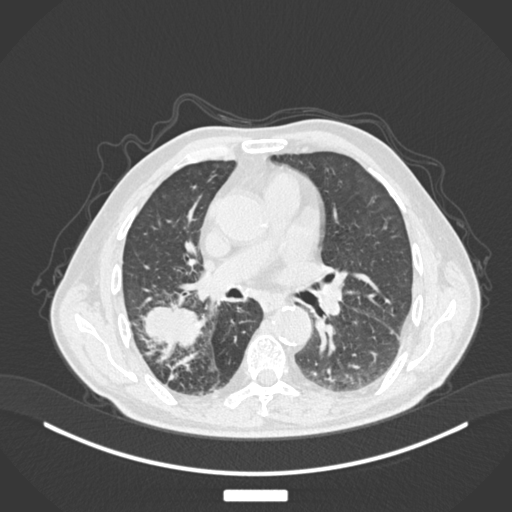
Chest CT, one axial slice; position 91 of 201 along the scan axis; reconstruction kernel B30f; lung window (W 1500 / L -600 HU); 512 × 512 image matrix, field of view 400 × 400 mm. Male patient, age 72 years. Case-level facts recorded for this patient, not image findings: clinical TNM (as recorded): T3 N2 M0.
Annotated regions visible in this slice (bounding box drawn by a radiologist):
- lung tumour (recorded histology: adenocarcinoma): bounding box [x1, y1, x2, y2] px = [136, 300, 203, 349]